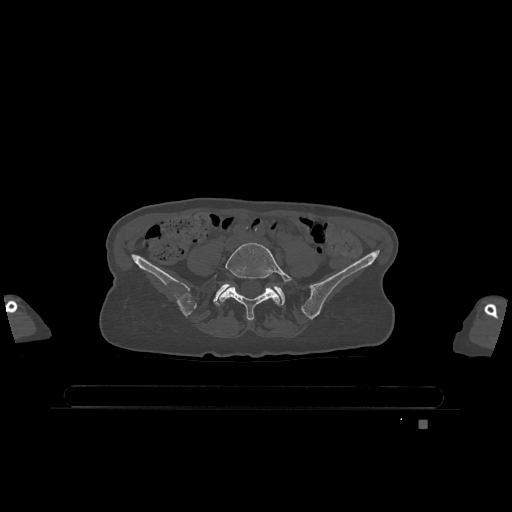
CT including the spine, one axial slice; slice 234 of 1317 in the series (ordered by position); bone window (W 1800 / L 400 HU); 0.5 mm slice thickness; 512 × 512 image matrix, field of view 500 × 500 mm. Female patient, age 74 years. From the clinical record (not read from this slice): primary cancer: lung.
Annotated regions visible in this slice (semi-automatic segmentation, software-assisted and operator-edited):
- L5 vertebra: bounding box (x1, y1, x2, y2) in pixels: (214, 243, 293, 321)